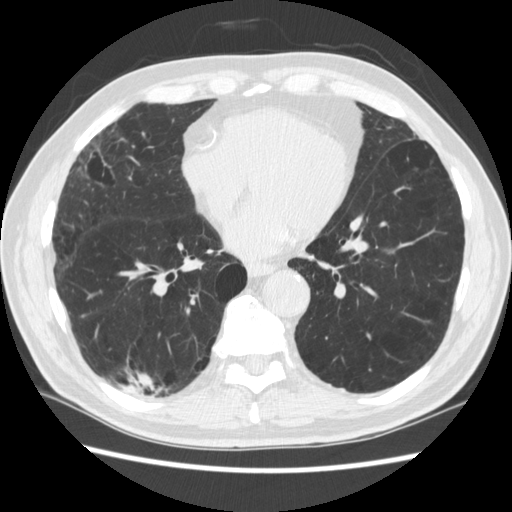
Low-dose screening chest CT, one axial slice; position 110 of 266 along the scan axis; reconstruction kernel STANDARD; 120 kVp; lung window (W 1500 / L -600 HU); 1.25 mm slice thickness; 512 × 512 image matrix, field of view 360 × 360 mm.
Annotated regions visible in this slice (expert manual segmentation):
- lesion 1 (tumor, upper lobe of right lung): bounding box (x1, y1, x2, y2) in pixels: (138, 375, 152, 386)